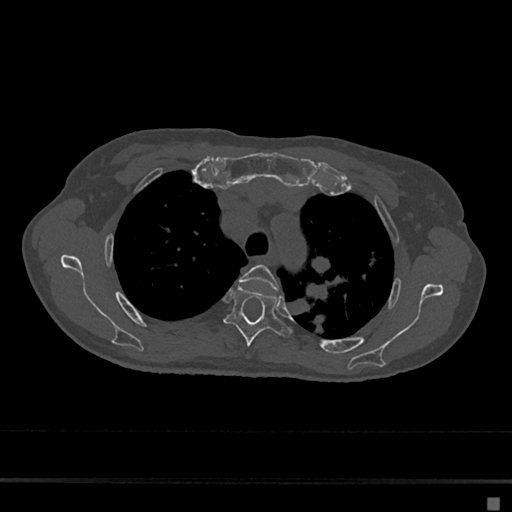
CT including the spine, one axial slice. Slice 508 of 797 in the series (ordered by position). Reconstruction kernel Br40s/3. Bone window (W 1800 / L 400 HU). 0.5 mm slice thickness. 512 × 512 image matrix. Patient: female, 68 years. From the clinical record (not read from this slice): primary cancer: renal.
Outlined on this slice (semi-automatic segmentation, software-assisted and operator-edited):
- T3 vertebra: bounding box [x1, y1, x2, y2] px = [239, 265, 279, 291]
- T4 vertebra: [224, 285, 292, 346]